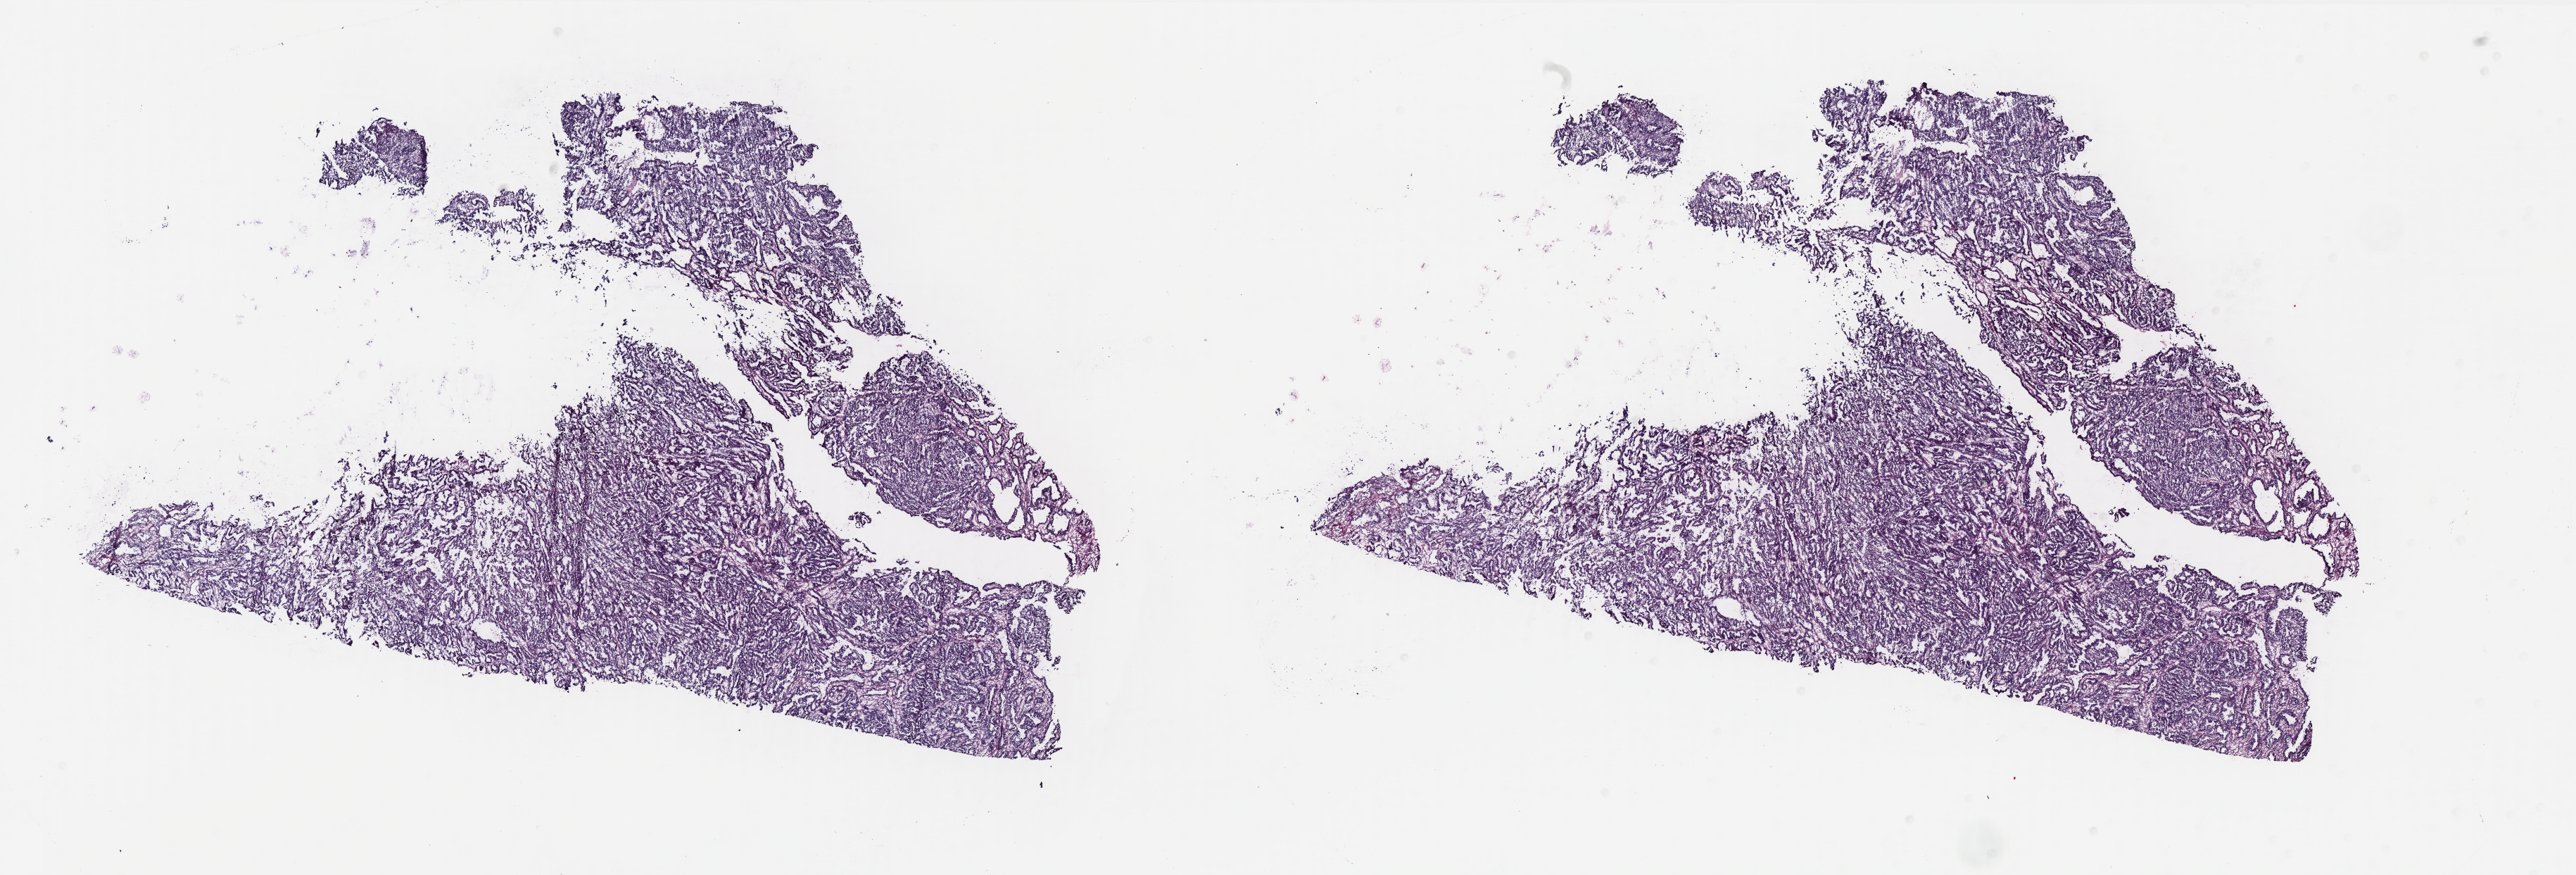
Digitized Hematoxylin and eosin (H&E) stained tissue section (whole slide), low-resolution overview of the scanned area, about 29.3 x 10.0 mm (from a 40x scan), frozen section, primary tumour sample from the uterus. Female, age 60 years at initial diagnosis. Histologic grade: G3 (poorly differentiated). Composition of this section per pathologist review: tumour cells 95%, tumour nuclei 90%, normal cells 5%, stromal cells 0%, necrosis 0%. Infiltration values recorded for this section: lymphocyte infiltration 0%, monocyte infiltration 0%, neutrophil infiltration 0%.
FIGO stage: IA. Lymph nodes positive (case pathology): 0 of 17 examined. Diagnosis: Serous cystadenocarcinoma, NOS (endometrium).